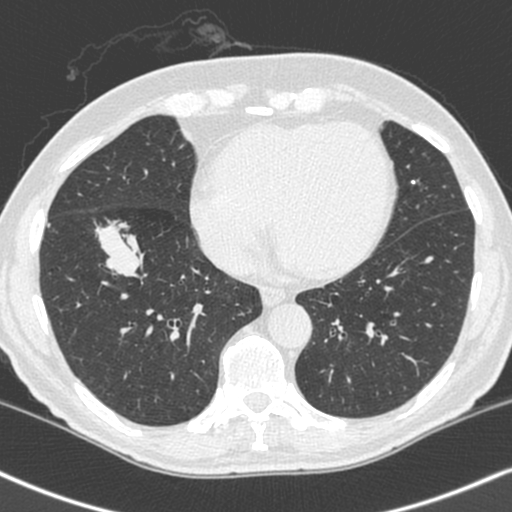
Chest CT (low-dose screening protocol), one axial image; baseline screening round; lung window (W 1500 / L -600 HU); 1.3 mm slice thickness; standard (soft-tissue) reconstruction kernel (C); 120 kVp; slice 153 of 248 in the series; 512 × 512 image matrix, field of view 323 × 323 mm. Male participant, aged 68 years at enrolment.
• Lesion marked by an expert reader, bounding box [x1, y1, x2, y2] px = [81, 211, 156, 281].
• Screening reader's record for this exam (one nodule recorded; not confirmed to be the boxed lesion): non-calcified nodule or mass ≥4 mm, right lower lobe, 34 × 17 mm, smooth margins, soft tissue attenuation.
• Official screen result: positive, change unspecified: nodule(s) >= 4 mm or enlarging nodule(s), mass(es), or other non-specific abnormalities suspicious for lung cancer.
• Later outcome: lung cancer diagnosed 24 days after this screen — combined small cell carcinoma, right lower lobe, stage IIIA (AJCC 6th edition), 41 mm at pathology.